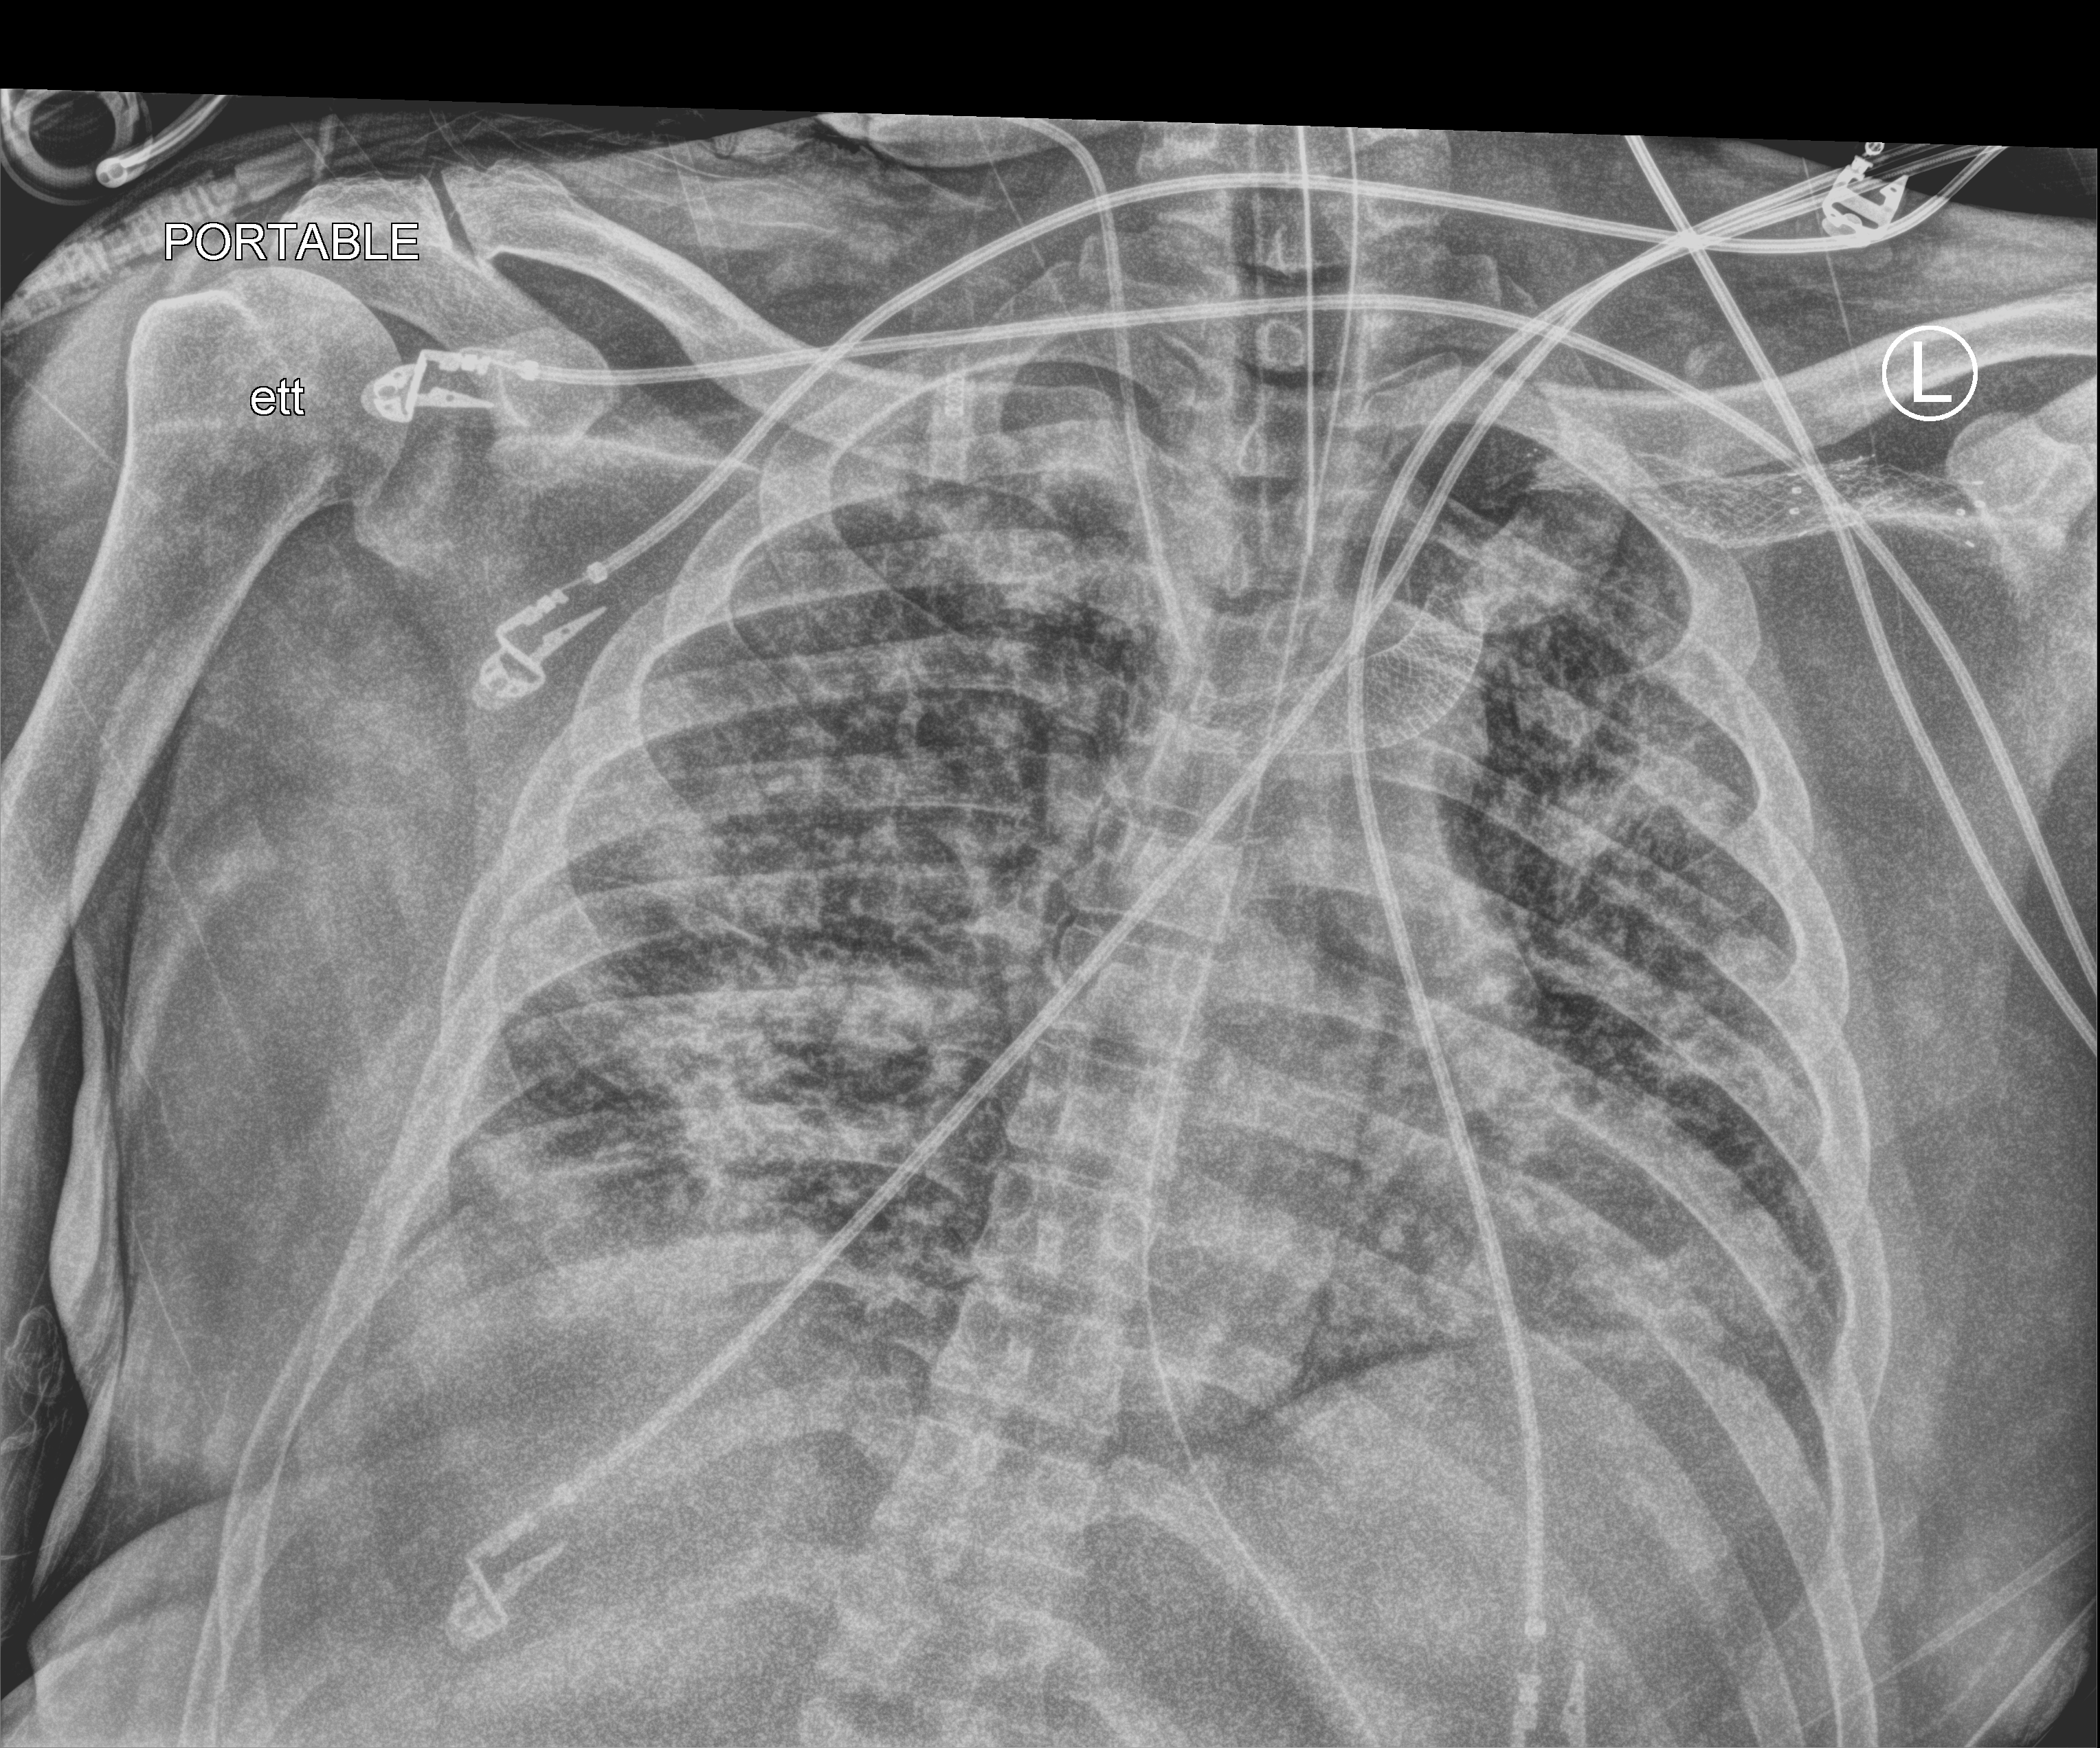
Bedside chest radiograph (computed radiography); anteroposterior (AP) projection. Male patient hospitalised with COVID-19, age 18–59 years.
Admission-level facts for this patient (not findings on this image; timing relative to this image not recorded): admitted to intensive care during this hospital stay: yes; chronic kidney disease (admission record): yes; mechanically ventilated during this hospital stay: yes.